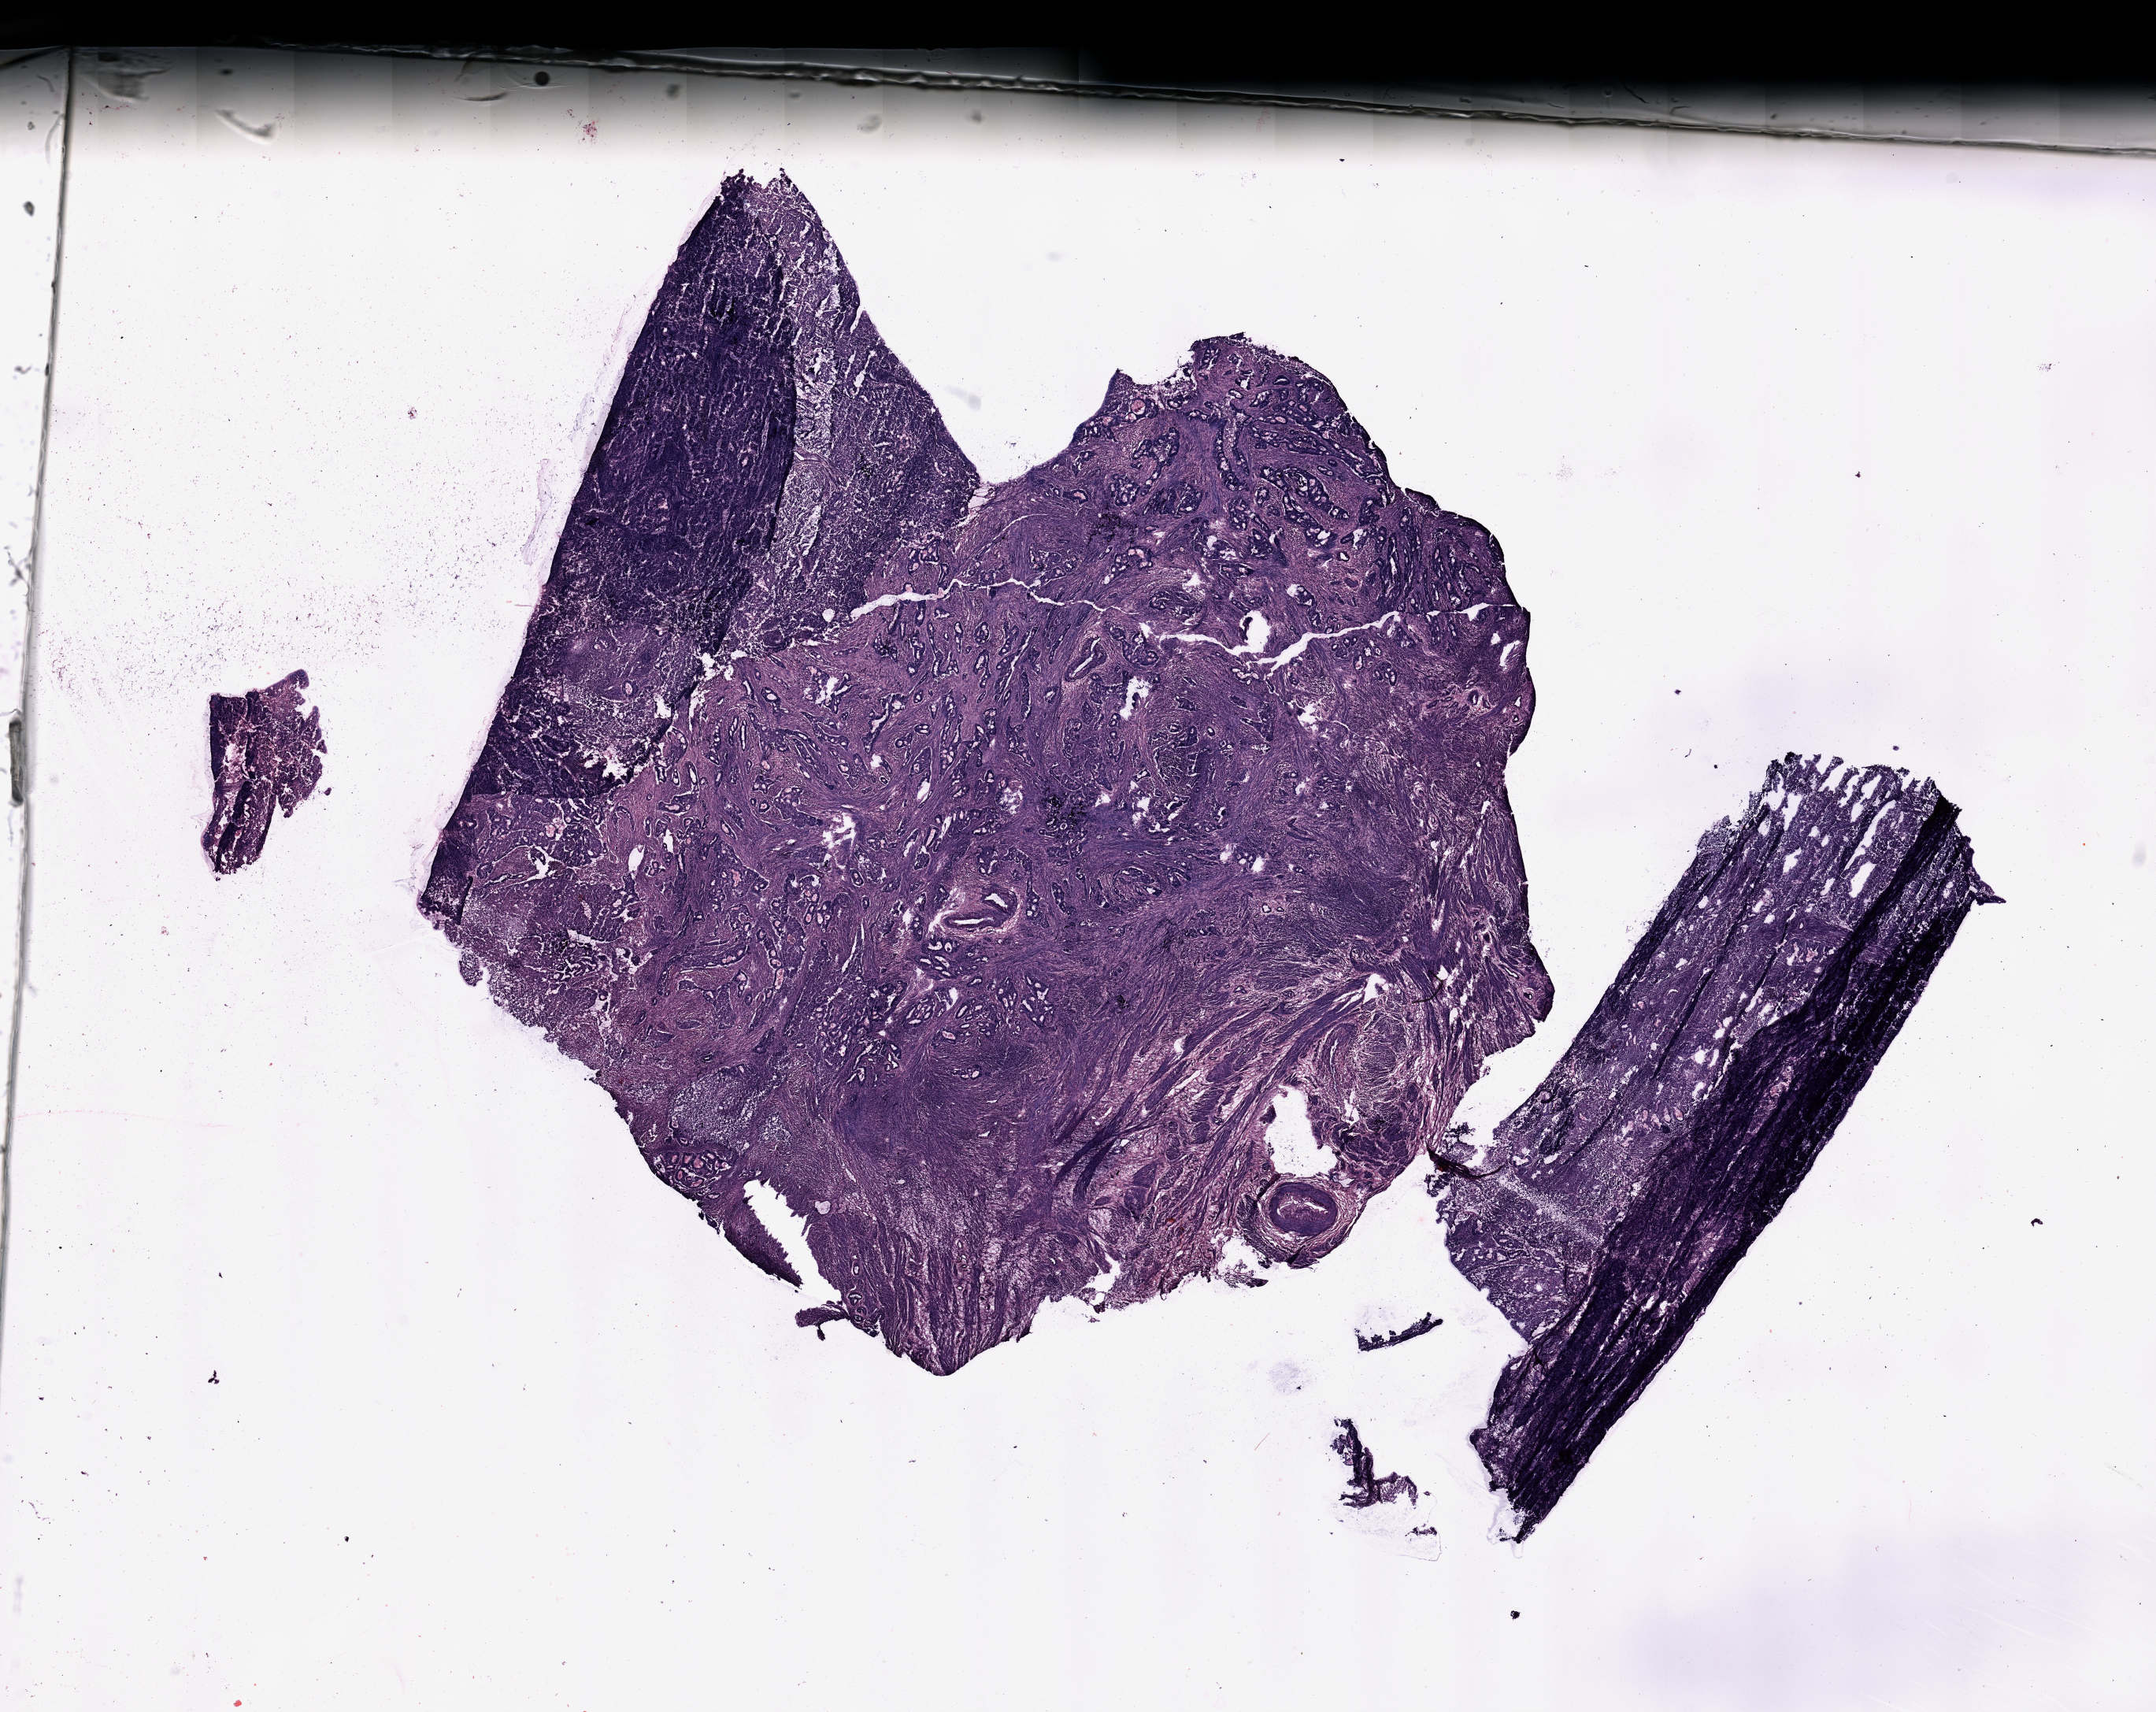
Digitized H&E tissue section (whole slide), a low-resolution overview of the entire scanned area, about 21.7 x 17.2 mm (acquisition: 20x scan), tumour tissue sample, uterus. Patient: female, age 62 years. Histologic grade: G2 (moderately differentiated).
Histologic diagnosis: Endometrioid adenocarcinoma, NOS. AJCC pathologic stage: I.